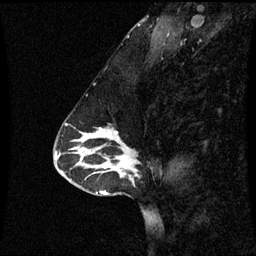
Breast MRI (dynamic contrast-enhanced), one sagittal slice. Position 26 of 60 along the scan axis. Dynamic contrast-enhanced series, image 2 of 3 at this slice position (ordered by acquisition). 1.5 T. TE 4.2 ms, TR 8.9 ms. 2 mm slice thickness. 256 × 256 image matrix, field of view 220 × 220 mm. Female patient, age 43 years. Case-level facts recorded for this patient, not image findings: setting: breast cancer imaged before/during neoadjuvant chemotherapy; receptor status: HR-positive, HER2-negative.
Annotated regions visible in this slice (semi-automatically segmented with operator editing):
- analysis volume of interest (the breast-tissue region the enhancement analysis was run in; not a lesion): bounding box [x1, y1, x2, y2] px = [84, 128, 140, 171]
- tumour enhancement mask (voxels above the 70 % enhancement threshold inside the analysis volume of interest): [100, 130, 119, 165]